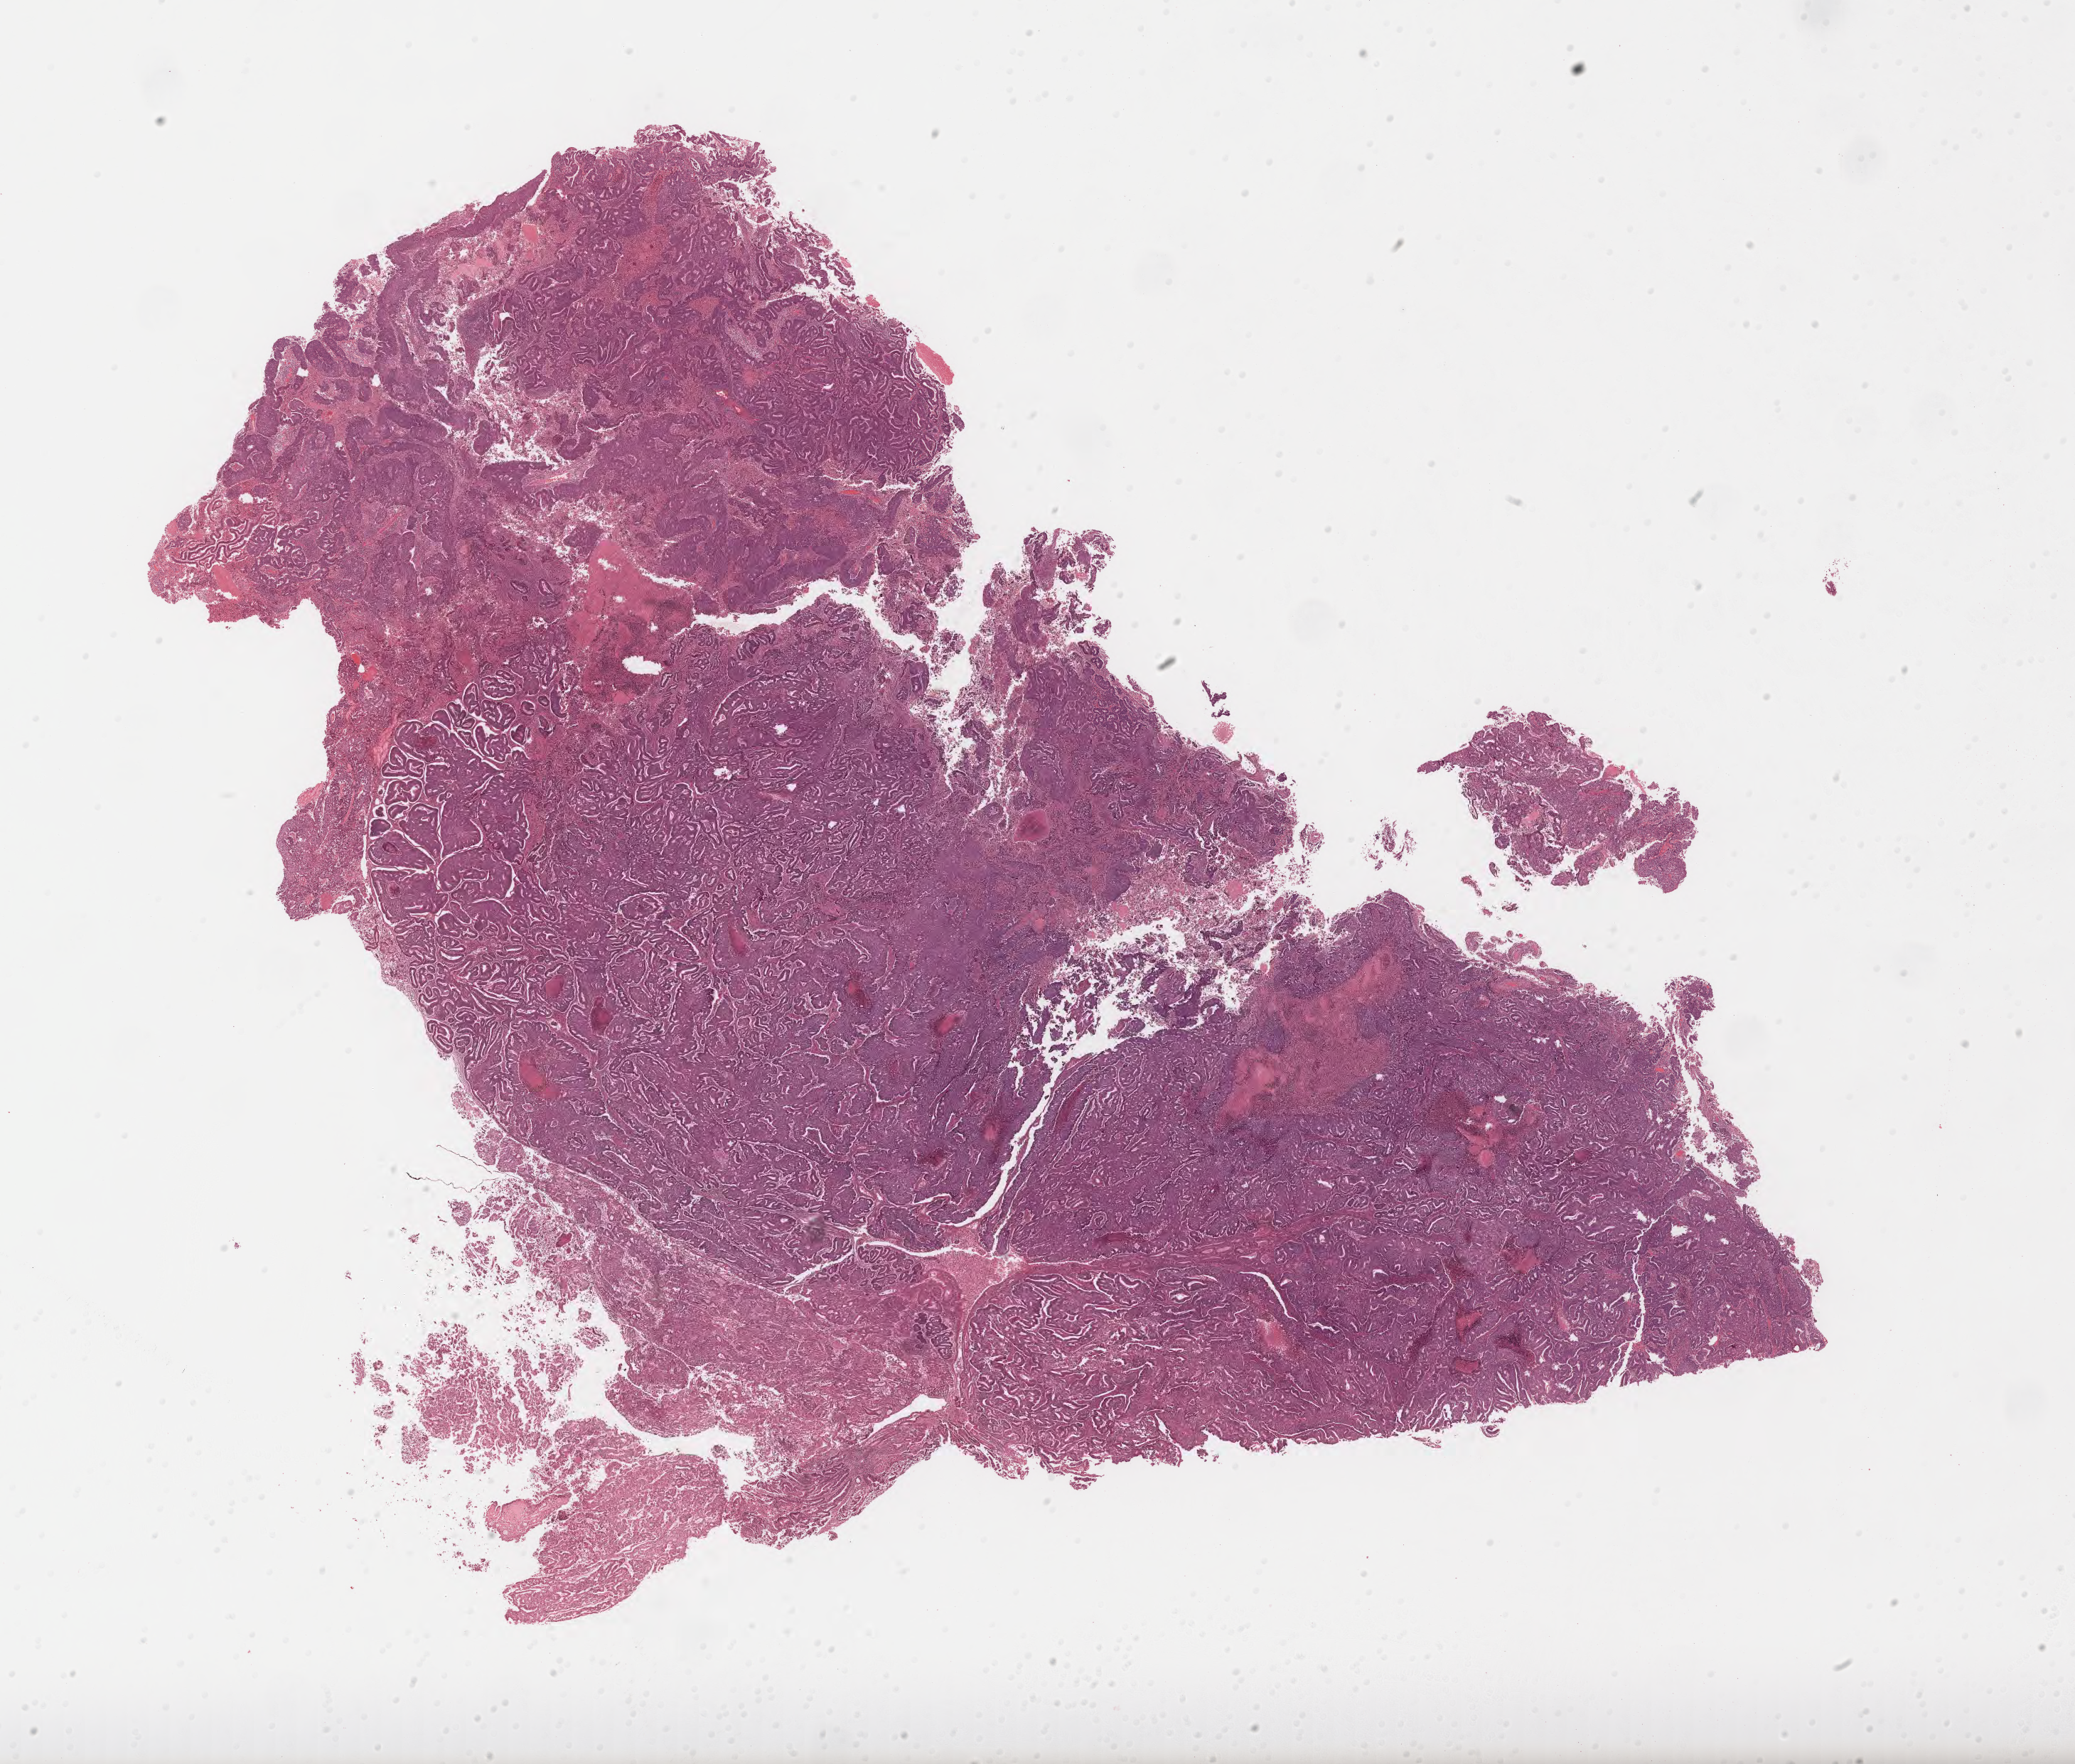
Digitized H&E-stained tissue section (whole slide) — a low-resolution overview of the entire scanned area, about 23.5 x 20.0 mm (slide scanned at 40x), formalin-fixed paraffin-embedded (FFPE) diagnostic section, primary tumour sample from the uterus. Female, age 80 years at initial diagnosis. Histologic grade: G3 (poorly differentiated).
* FIGO stage: IA
* pathologic diagnosis: Endometrioid adenocarcinoma, NOS (endometrium)